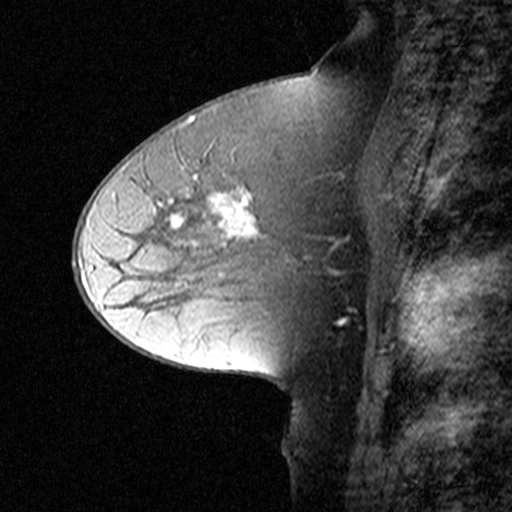
Breast MRI (dynamic contrast-enhanced), one sagittal slice; position 25 of 44 along the scan axis; dynamic contrast-enhanced study with each time point stored as its own series, time point 2 of 3 at this slice position (early post-contrast, ordered by acquisition time); 1.5 T; TE 4.5 ms, TR 11 ms; 3 mm slice thickness; 512 × 512 image matrix. Female patient, age 50 years. Case-level facts recorded for this patient, not image findings: setting: breast cancer imaged before/during neoadjuvant chemotherapy; receptor status: HR-positive, HER2-negative.
Outlined on this slice (semi-automatic segmentation, software-assisted and operator-edited):
- analysis volume of interest (the breast-tissue region the enhancement analysis was run in; not a lesion): box from (x=126, y=162) to (x=329, y=291) px
- tumour enhancement mask (voxels above the 90 % enhancement threshold inside the analysis volume of interest): (x=171, y=189)–(x=259, y=239)